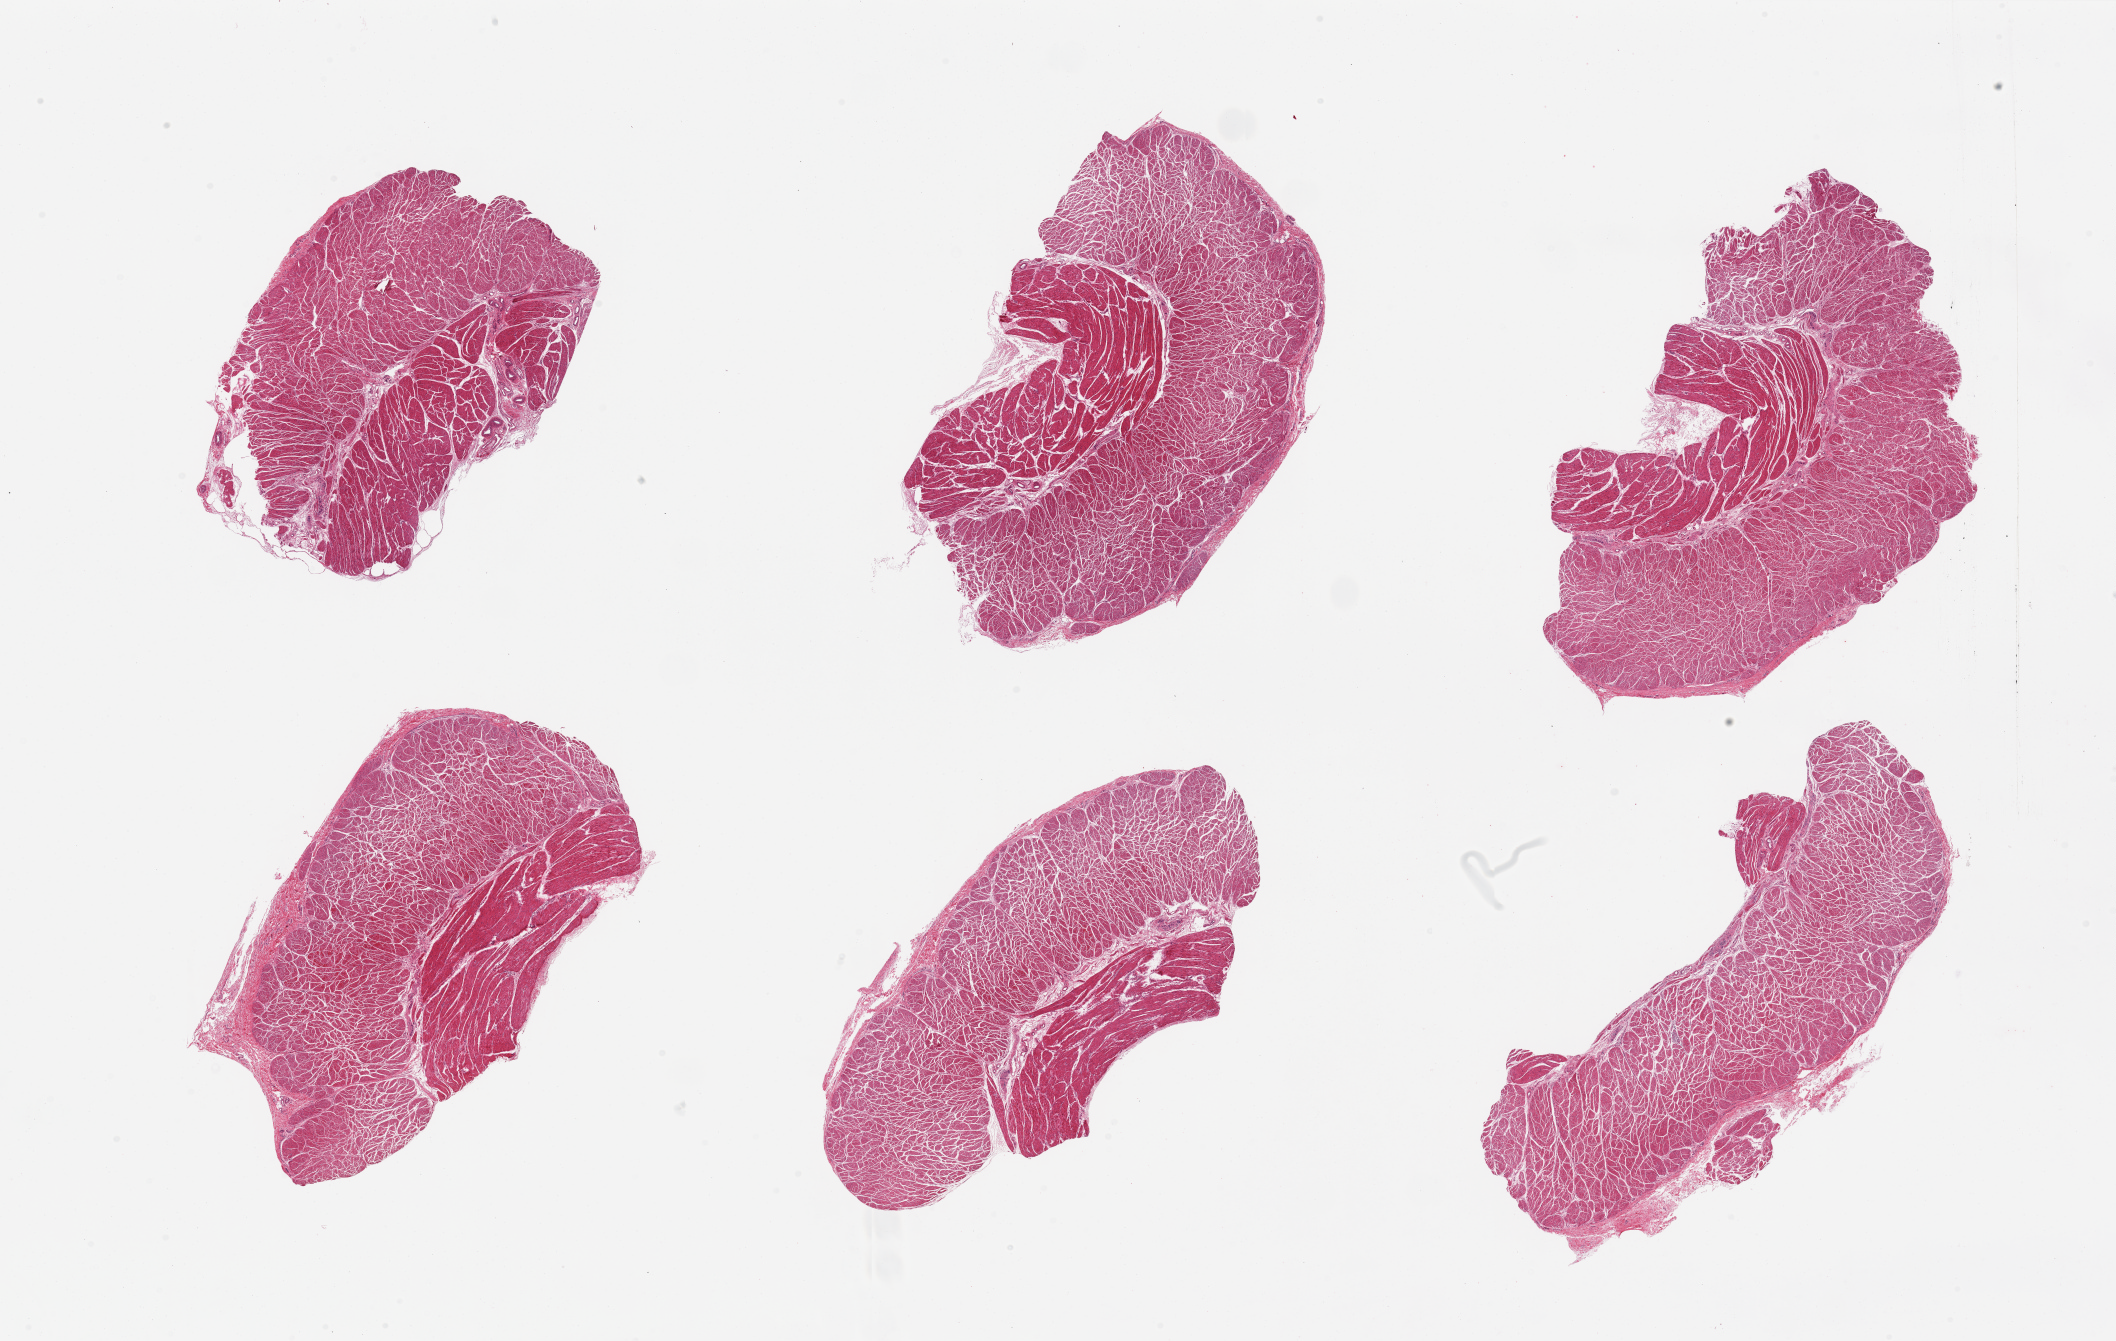
Whole-slide image, H&E stain, brightfield, a low-resolution overview of the entire scanned area, about 33.5 x 21.2 mm (from a 20x scan). PAXgene-fixed paraffin-embedded (PFPE) section. Section of esophageal muscle (target tissue). Tissue donor sample. Donor: male.
- reviewer comment on this tissue sample: 6 pieces, from 7x4 to 9x5mm; well trimmed